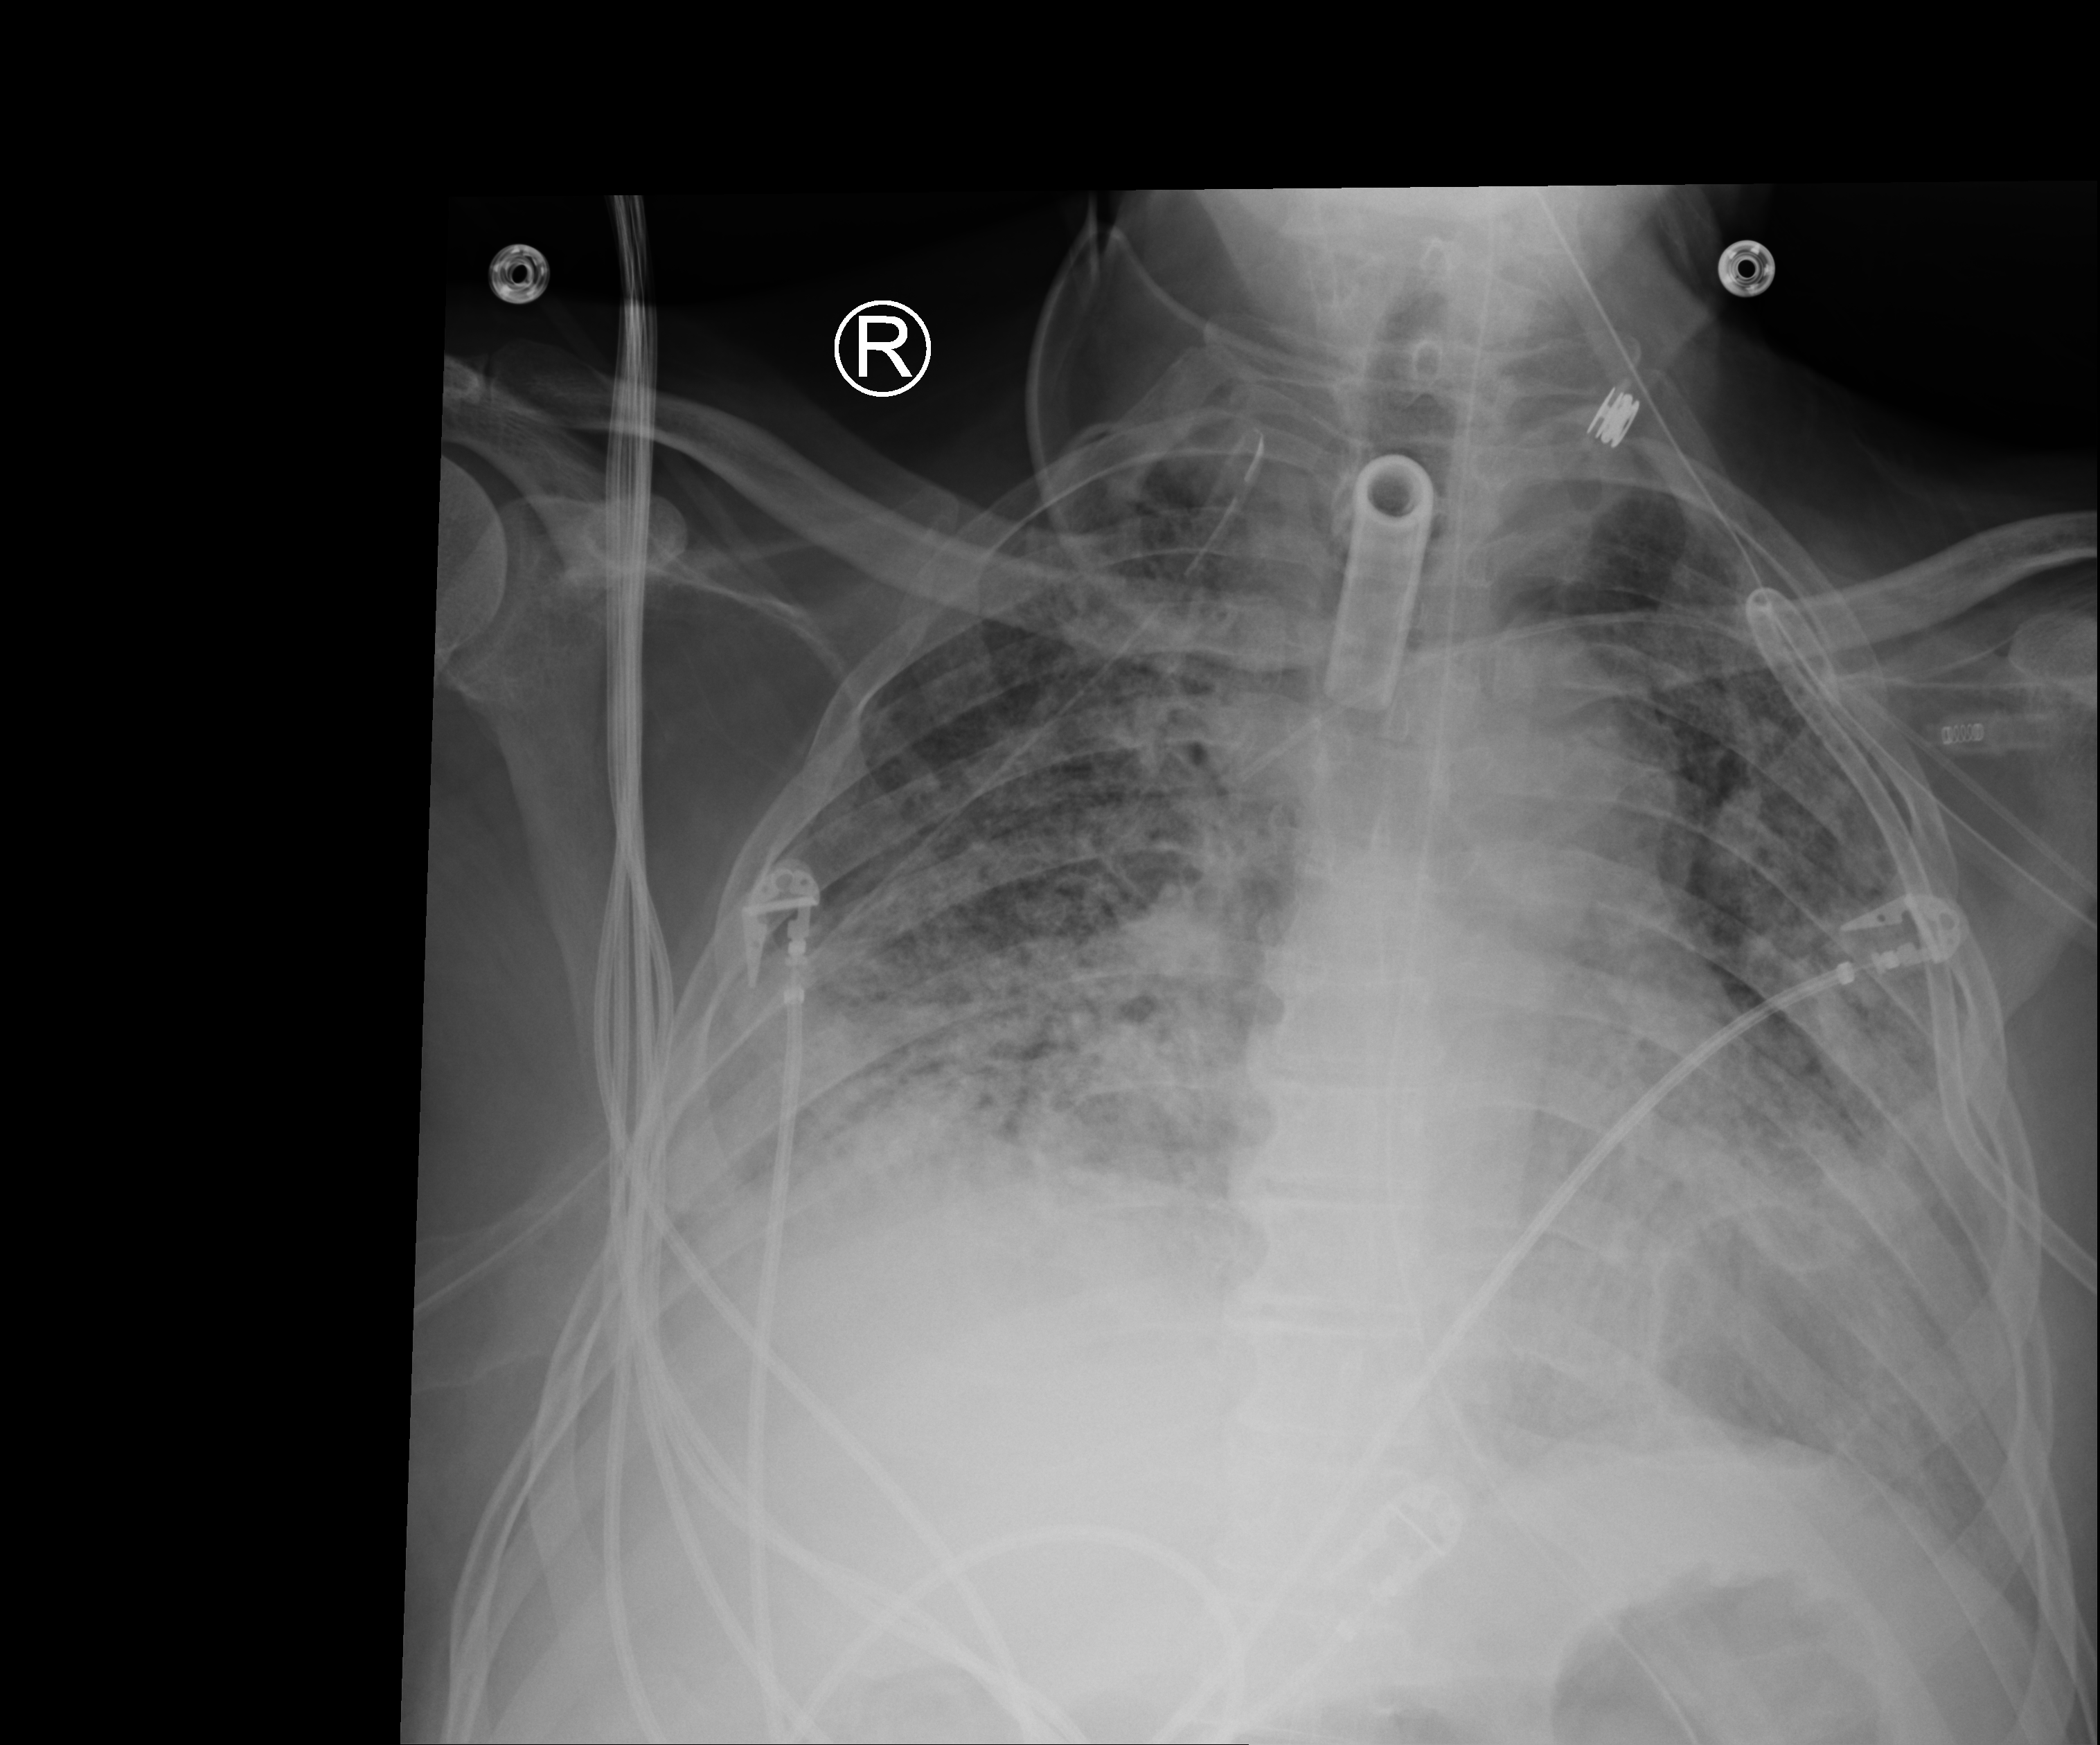
Bedside chest radiograph (computed radiography); anteroposterior (AP) projection. Patient hospitalised with COVID-19; male, aged 18–59 years.
Hospital-stay facts (about this admission, not read from this image; timing relative to this image not recorded):
- smoking status (admission record): never